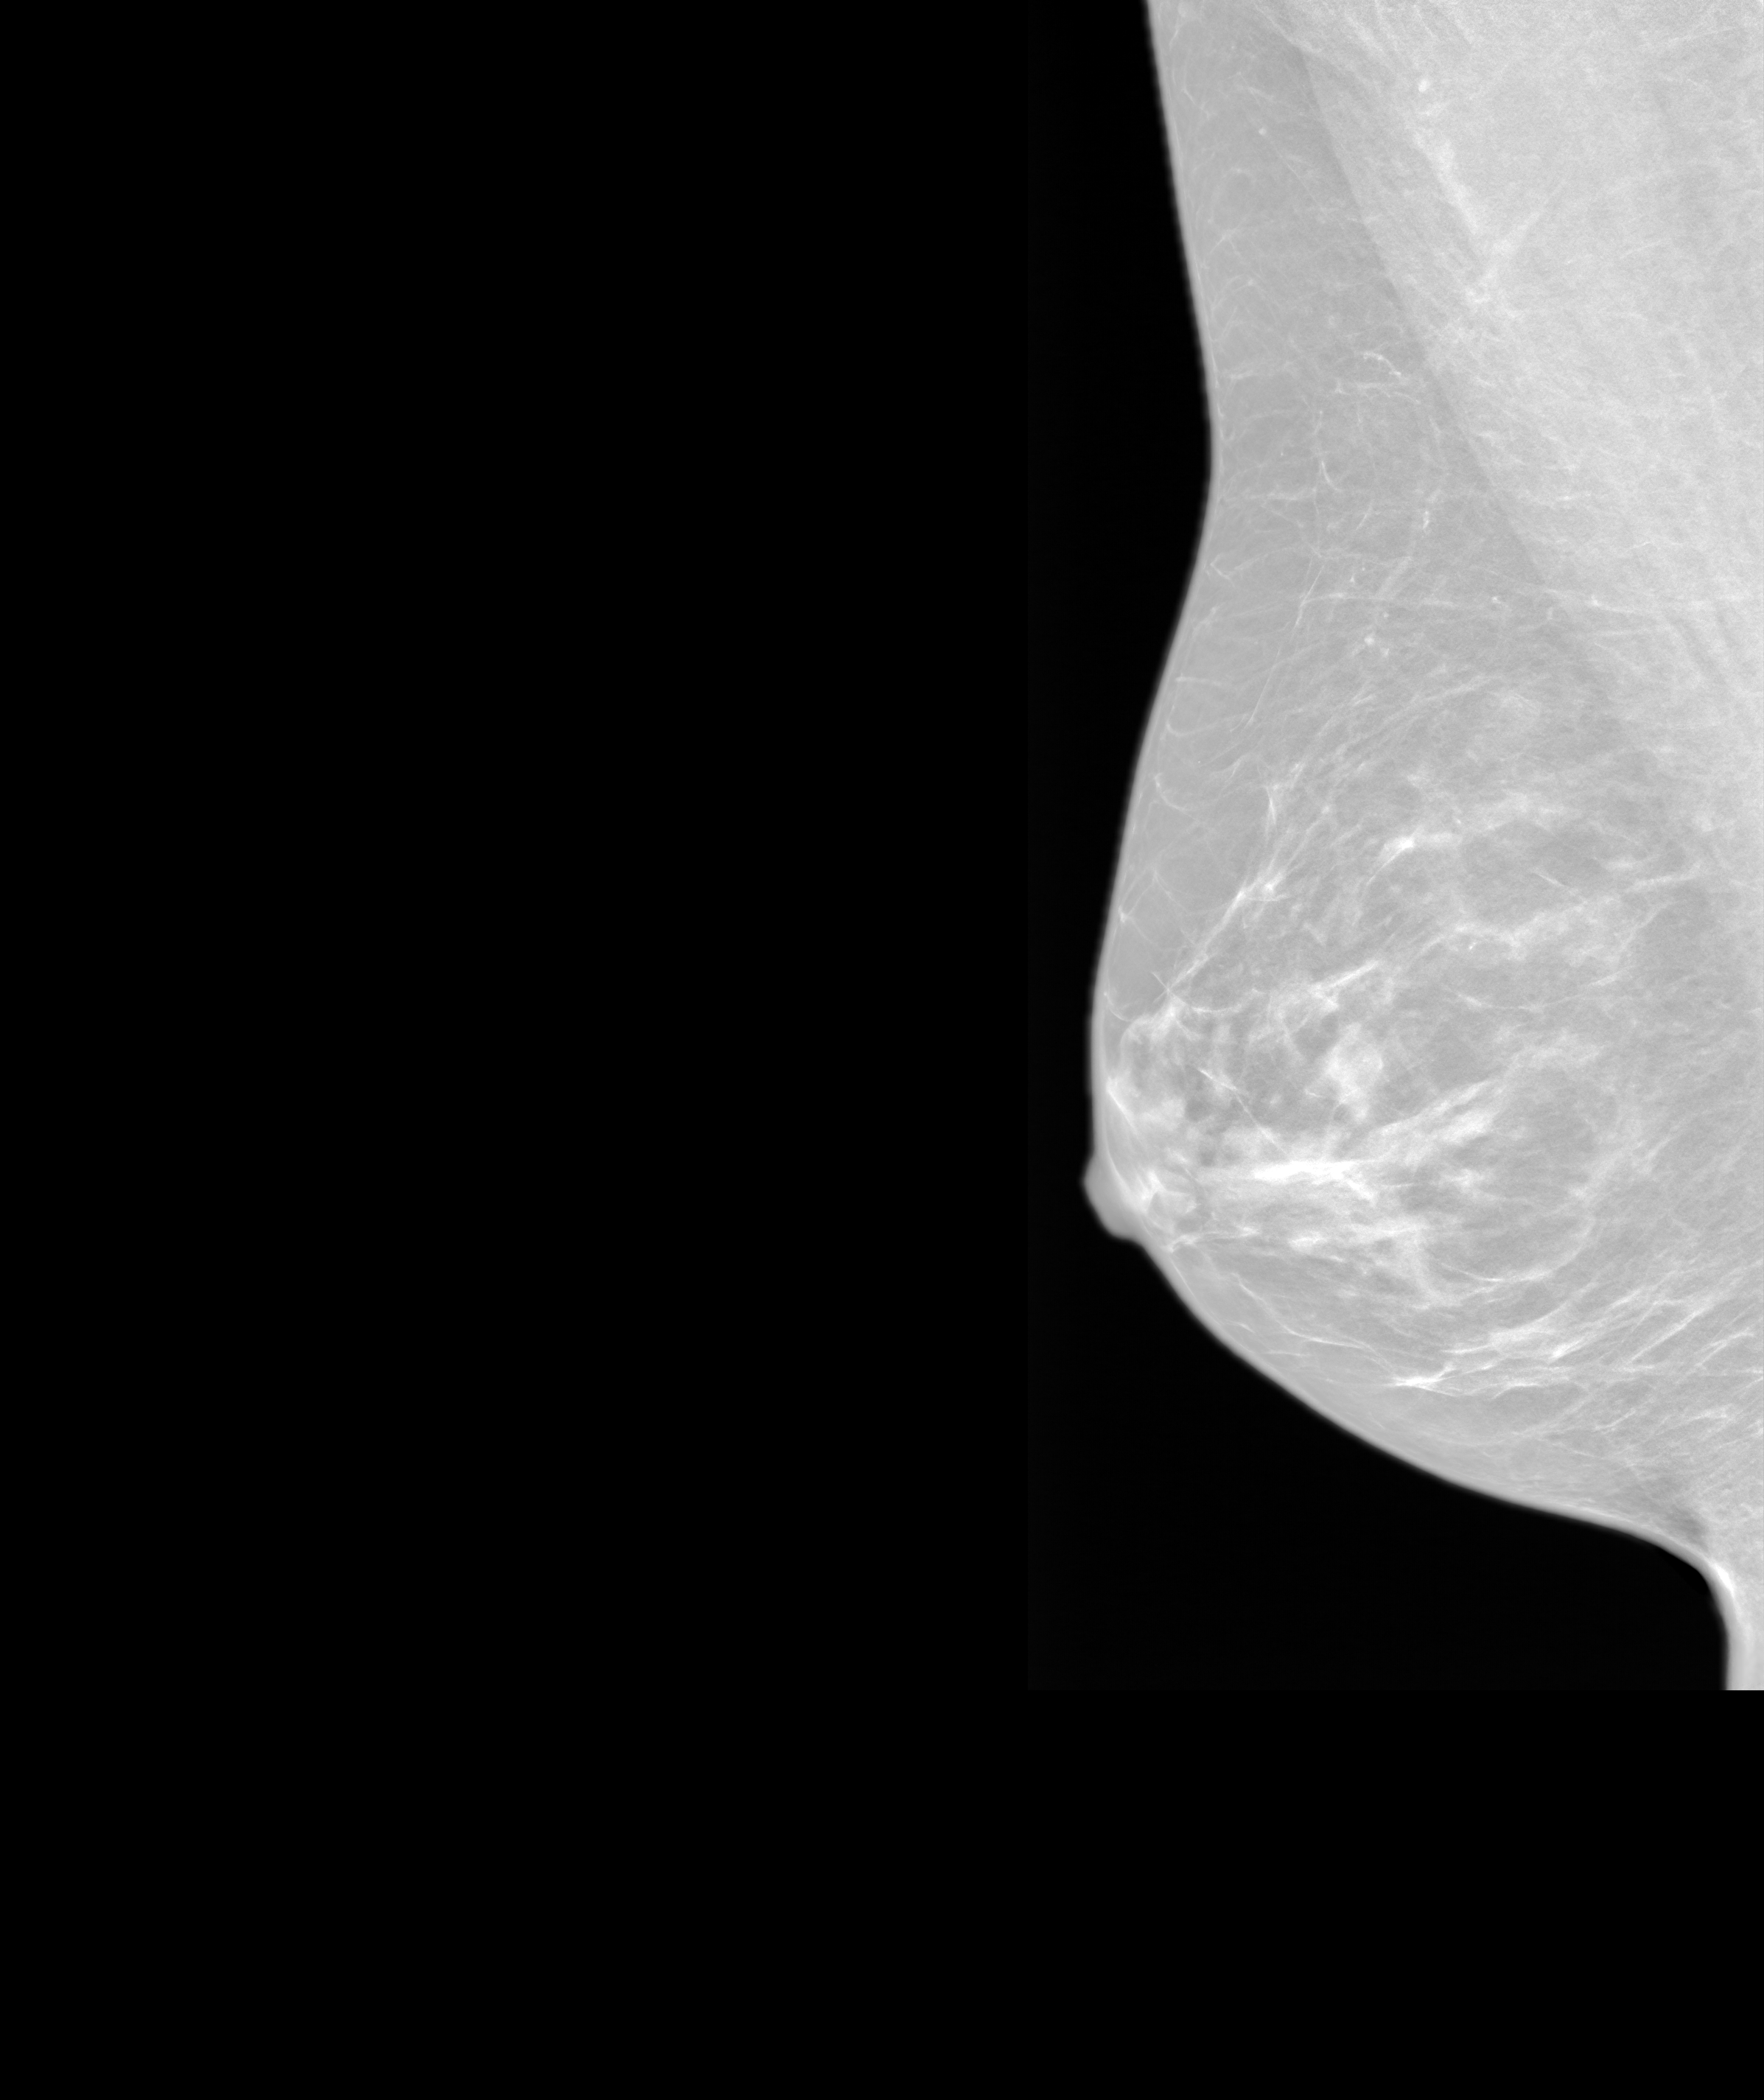
Annual screening mammography examination. Female patient, age 58 years.
Image type: synthesized 2-D view from tomosynthesis. Breast: right. Projection: mediolateral oblique (MLO) view.